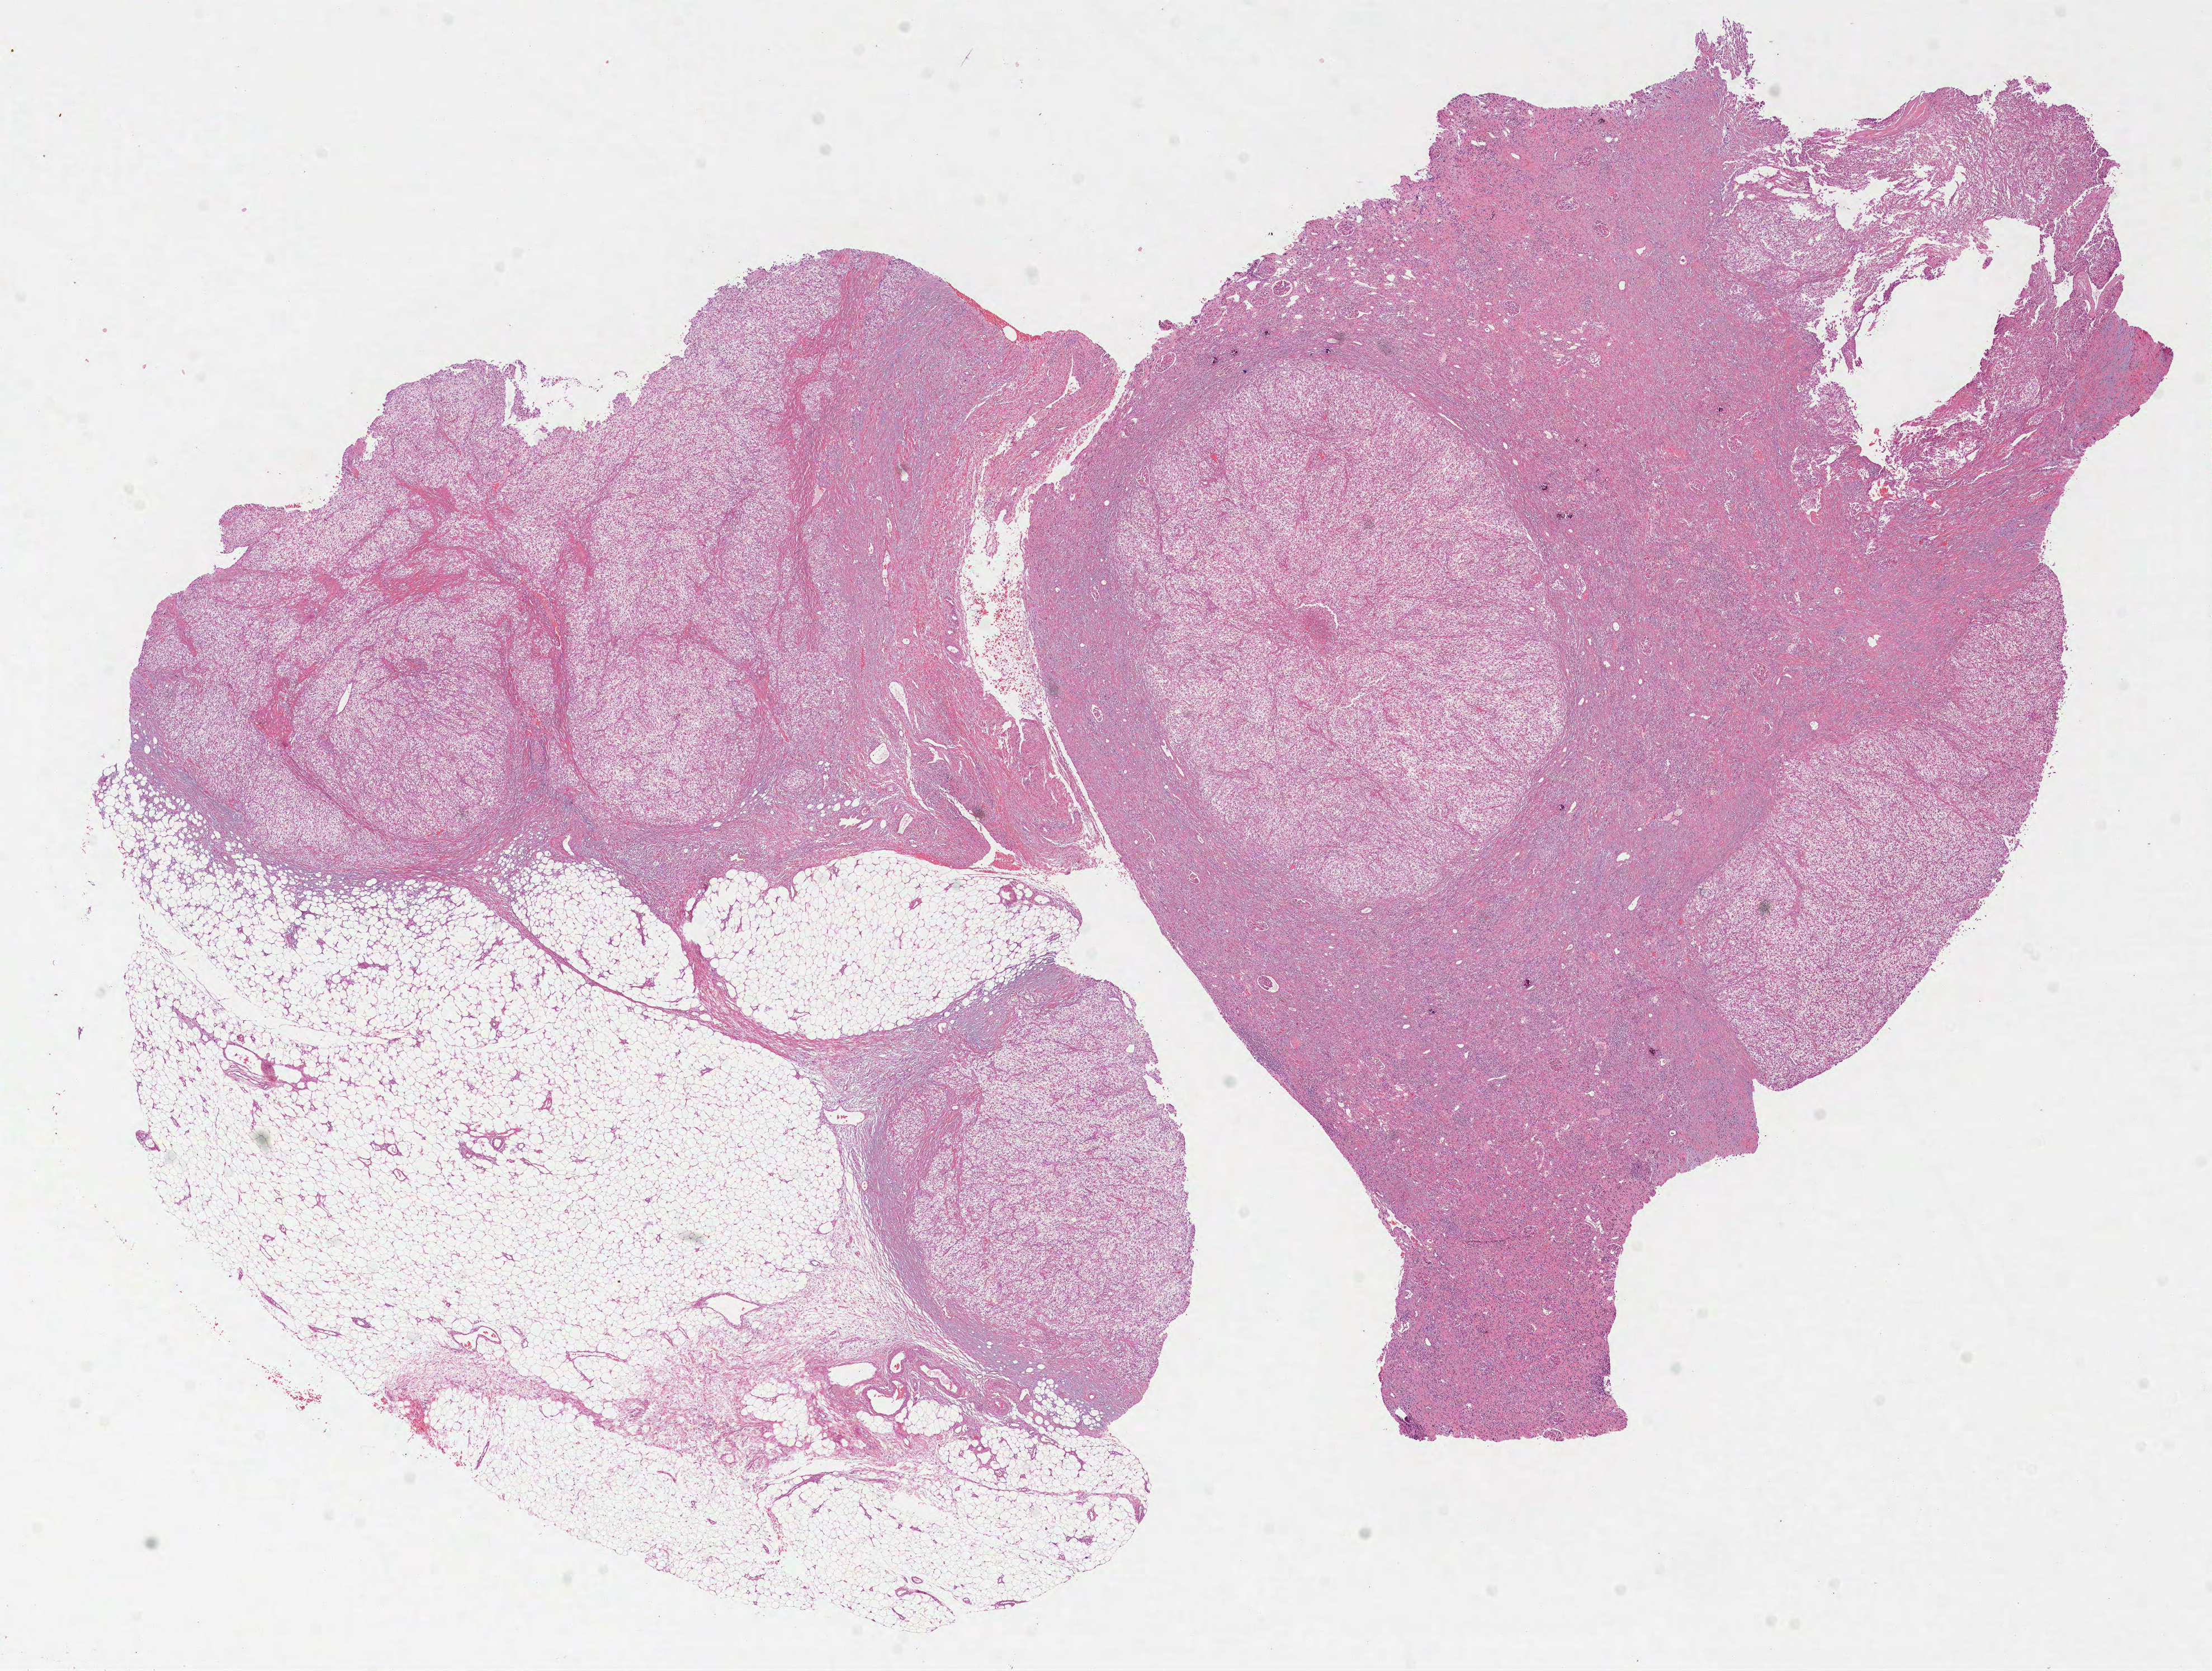
Whole-slide histology image, H&E — shown as a low-resolution overview of the whole scanned area (about 16.0 x 12.1 mm). Formalin-fixed paraffin-embedded (FFPE) diagnostic section. Sample: primary tumour, kidney. Female, age 76 years at initial diagnosis. Histologic grade: G2 (moderately differentiated).
AJCC pathologic stage: III. Diagnosis: Clear cell adenocarcinoma, NOS. Lymph nodes positive (case pathology): 1 of 1 examined.